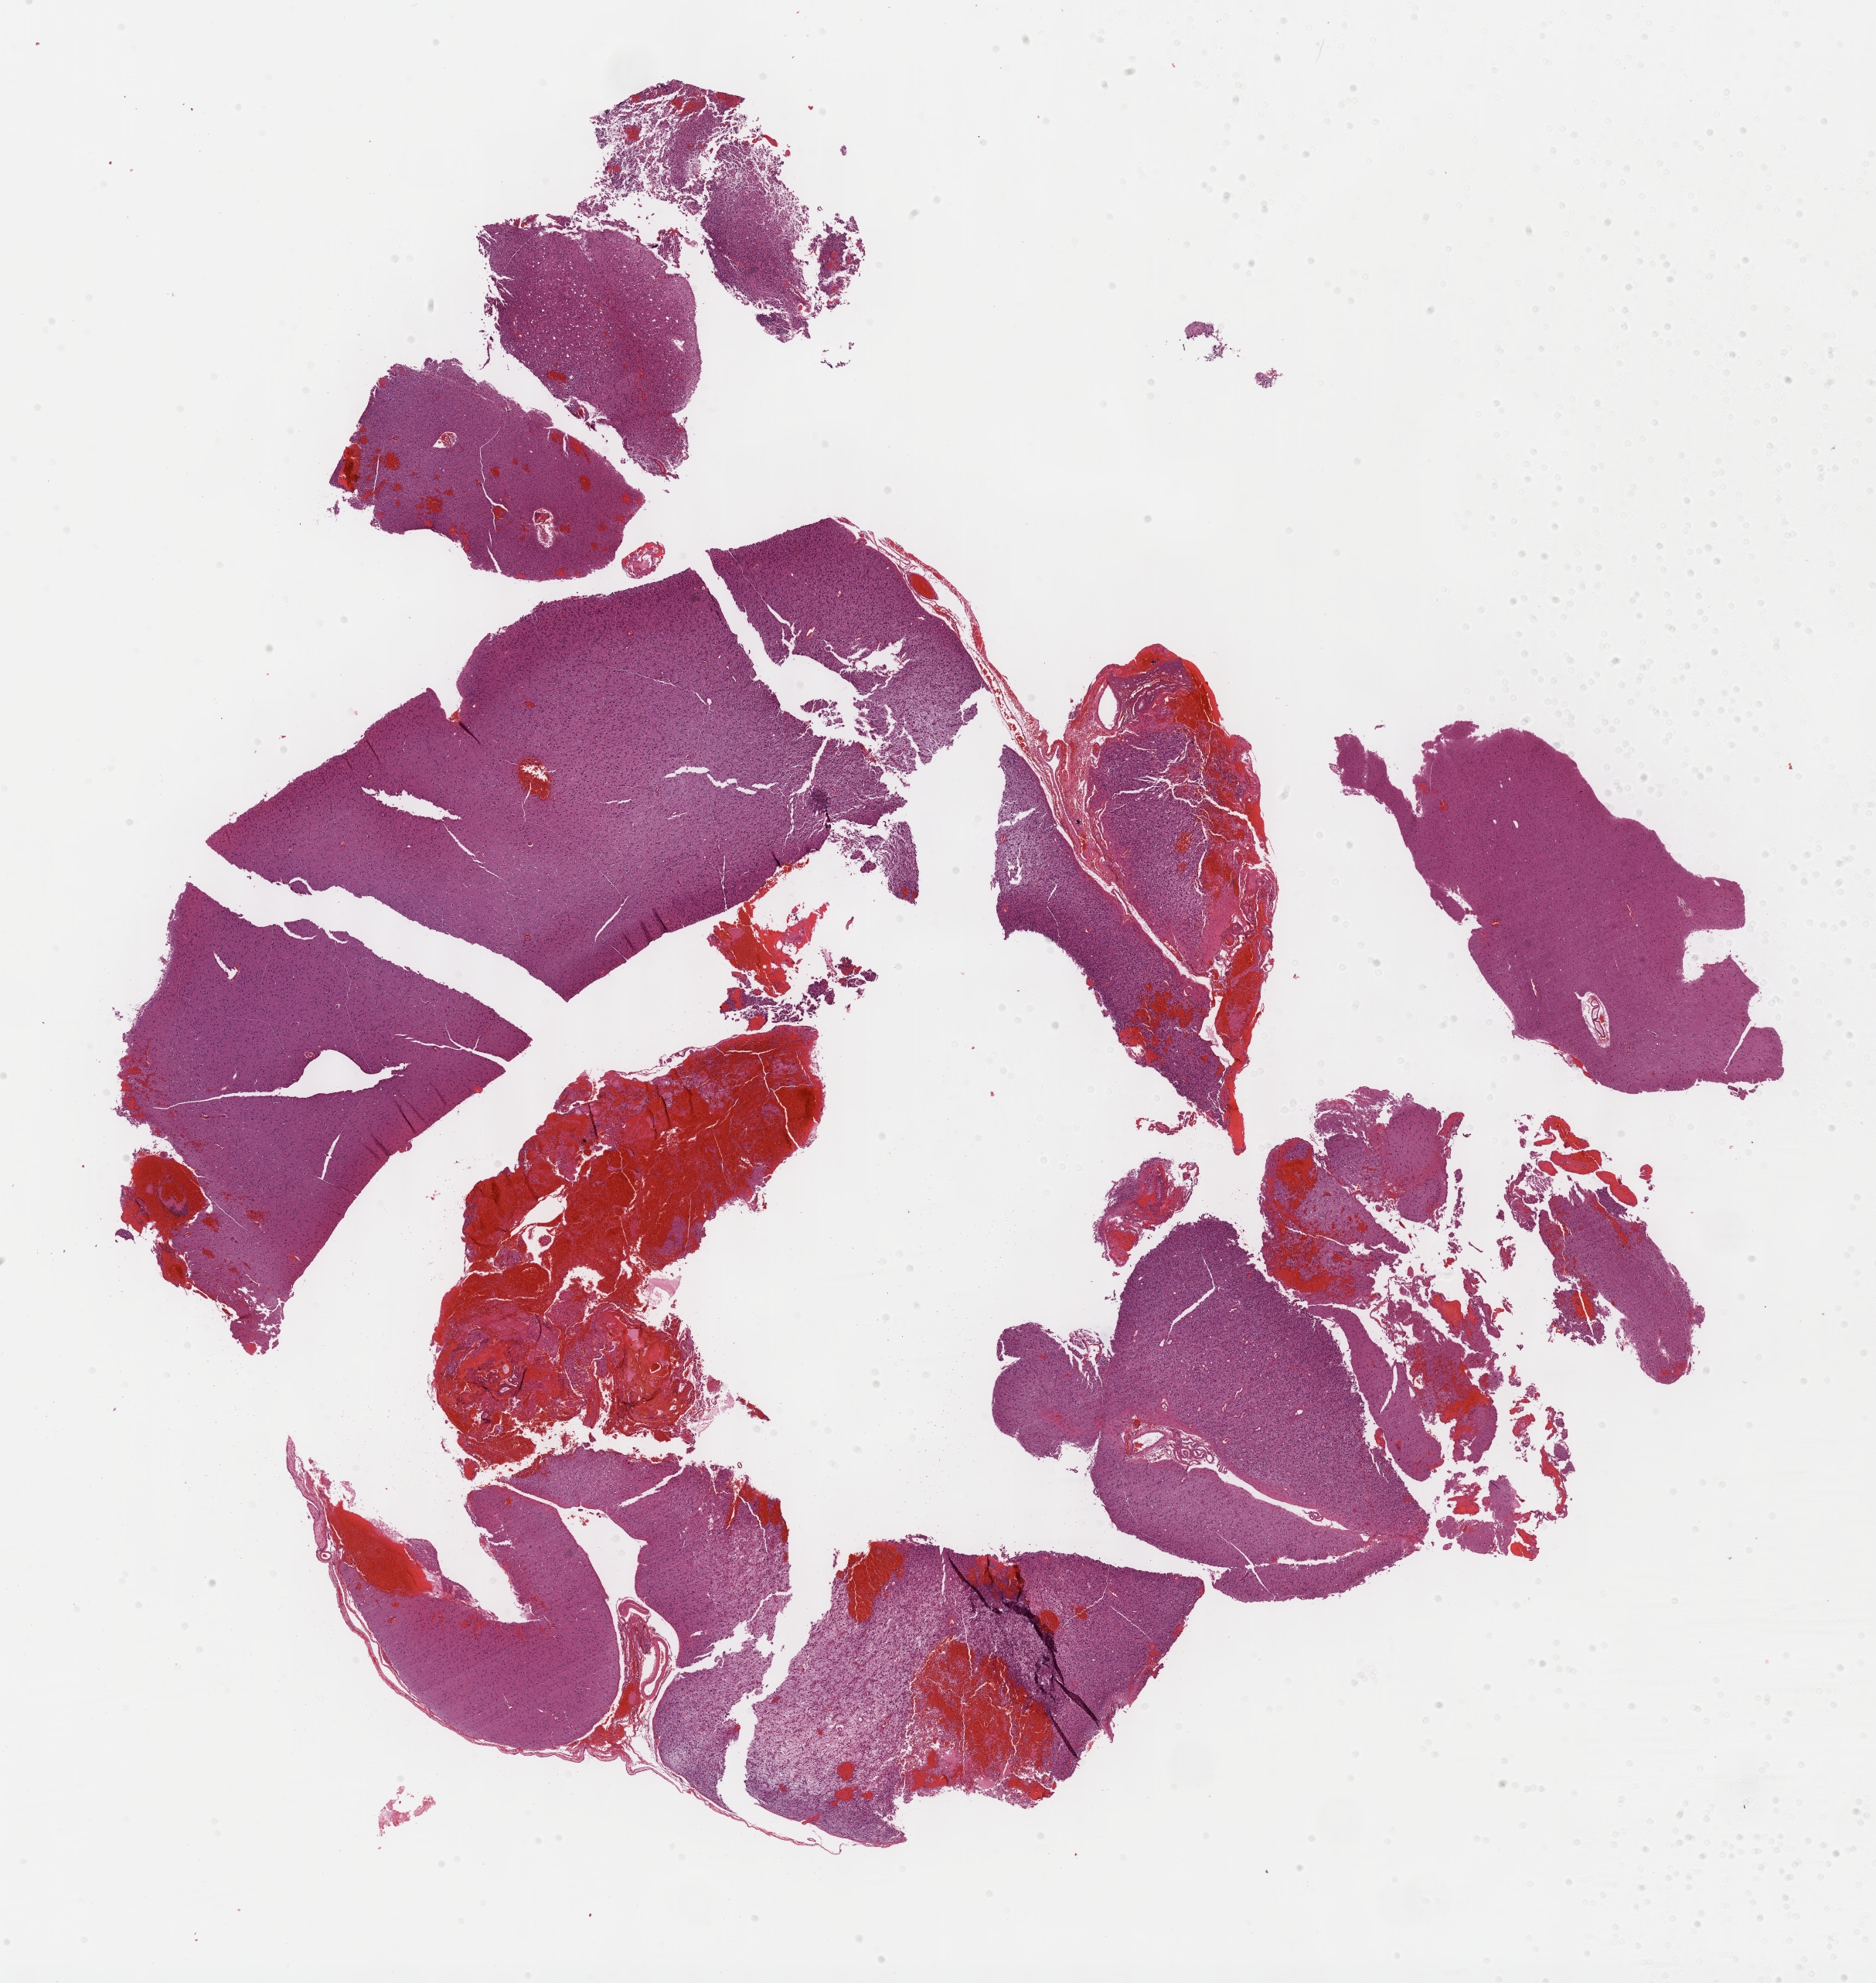
Hematoxylin and eosin (H&E) stained whole-slide image — shown as a low-resolution overview of the whole scanned area (about 19.6 x 20.7 mm, acquisition: 40x scan), FFPE section, primary tumour sample from the brain. Male patient; age at initial diagnosis 14 years. Histologic grade: G2 (moderately differentiated).
Diagnosis: Mixed glioma (cerebrum).